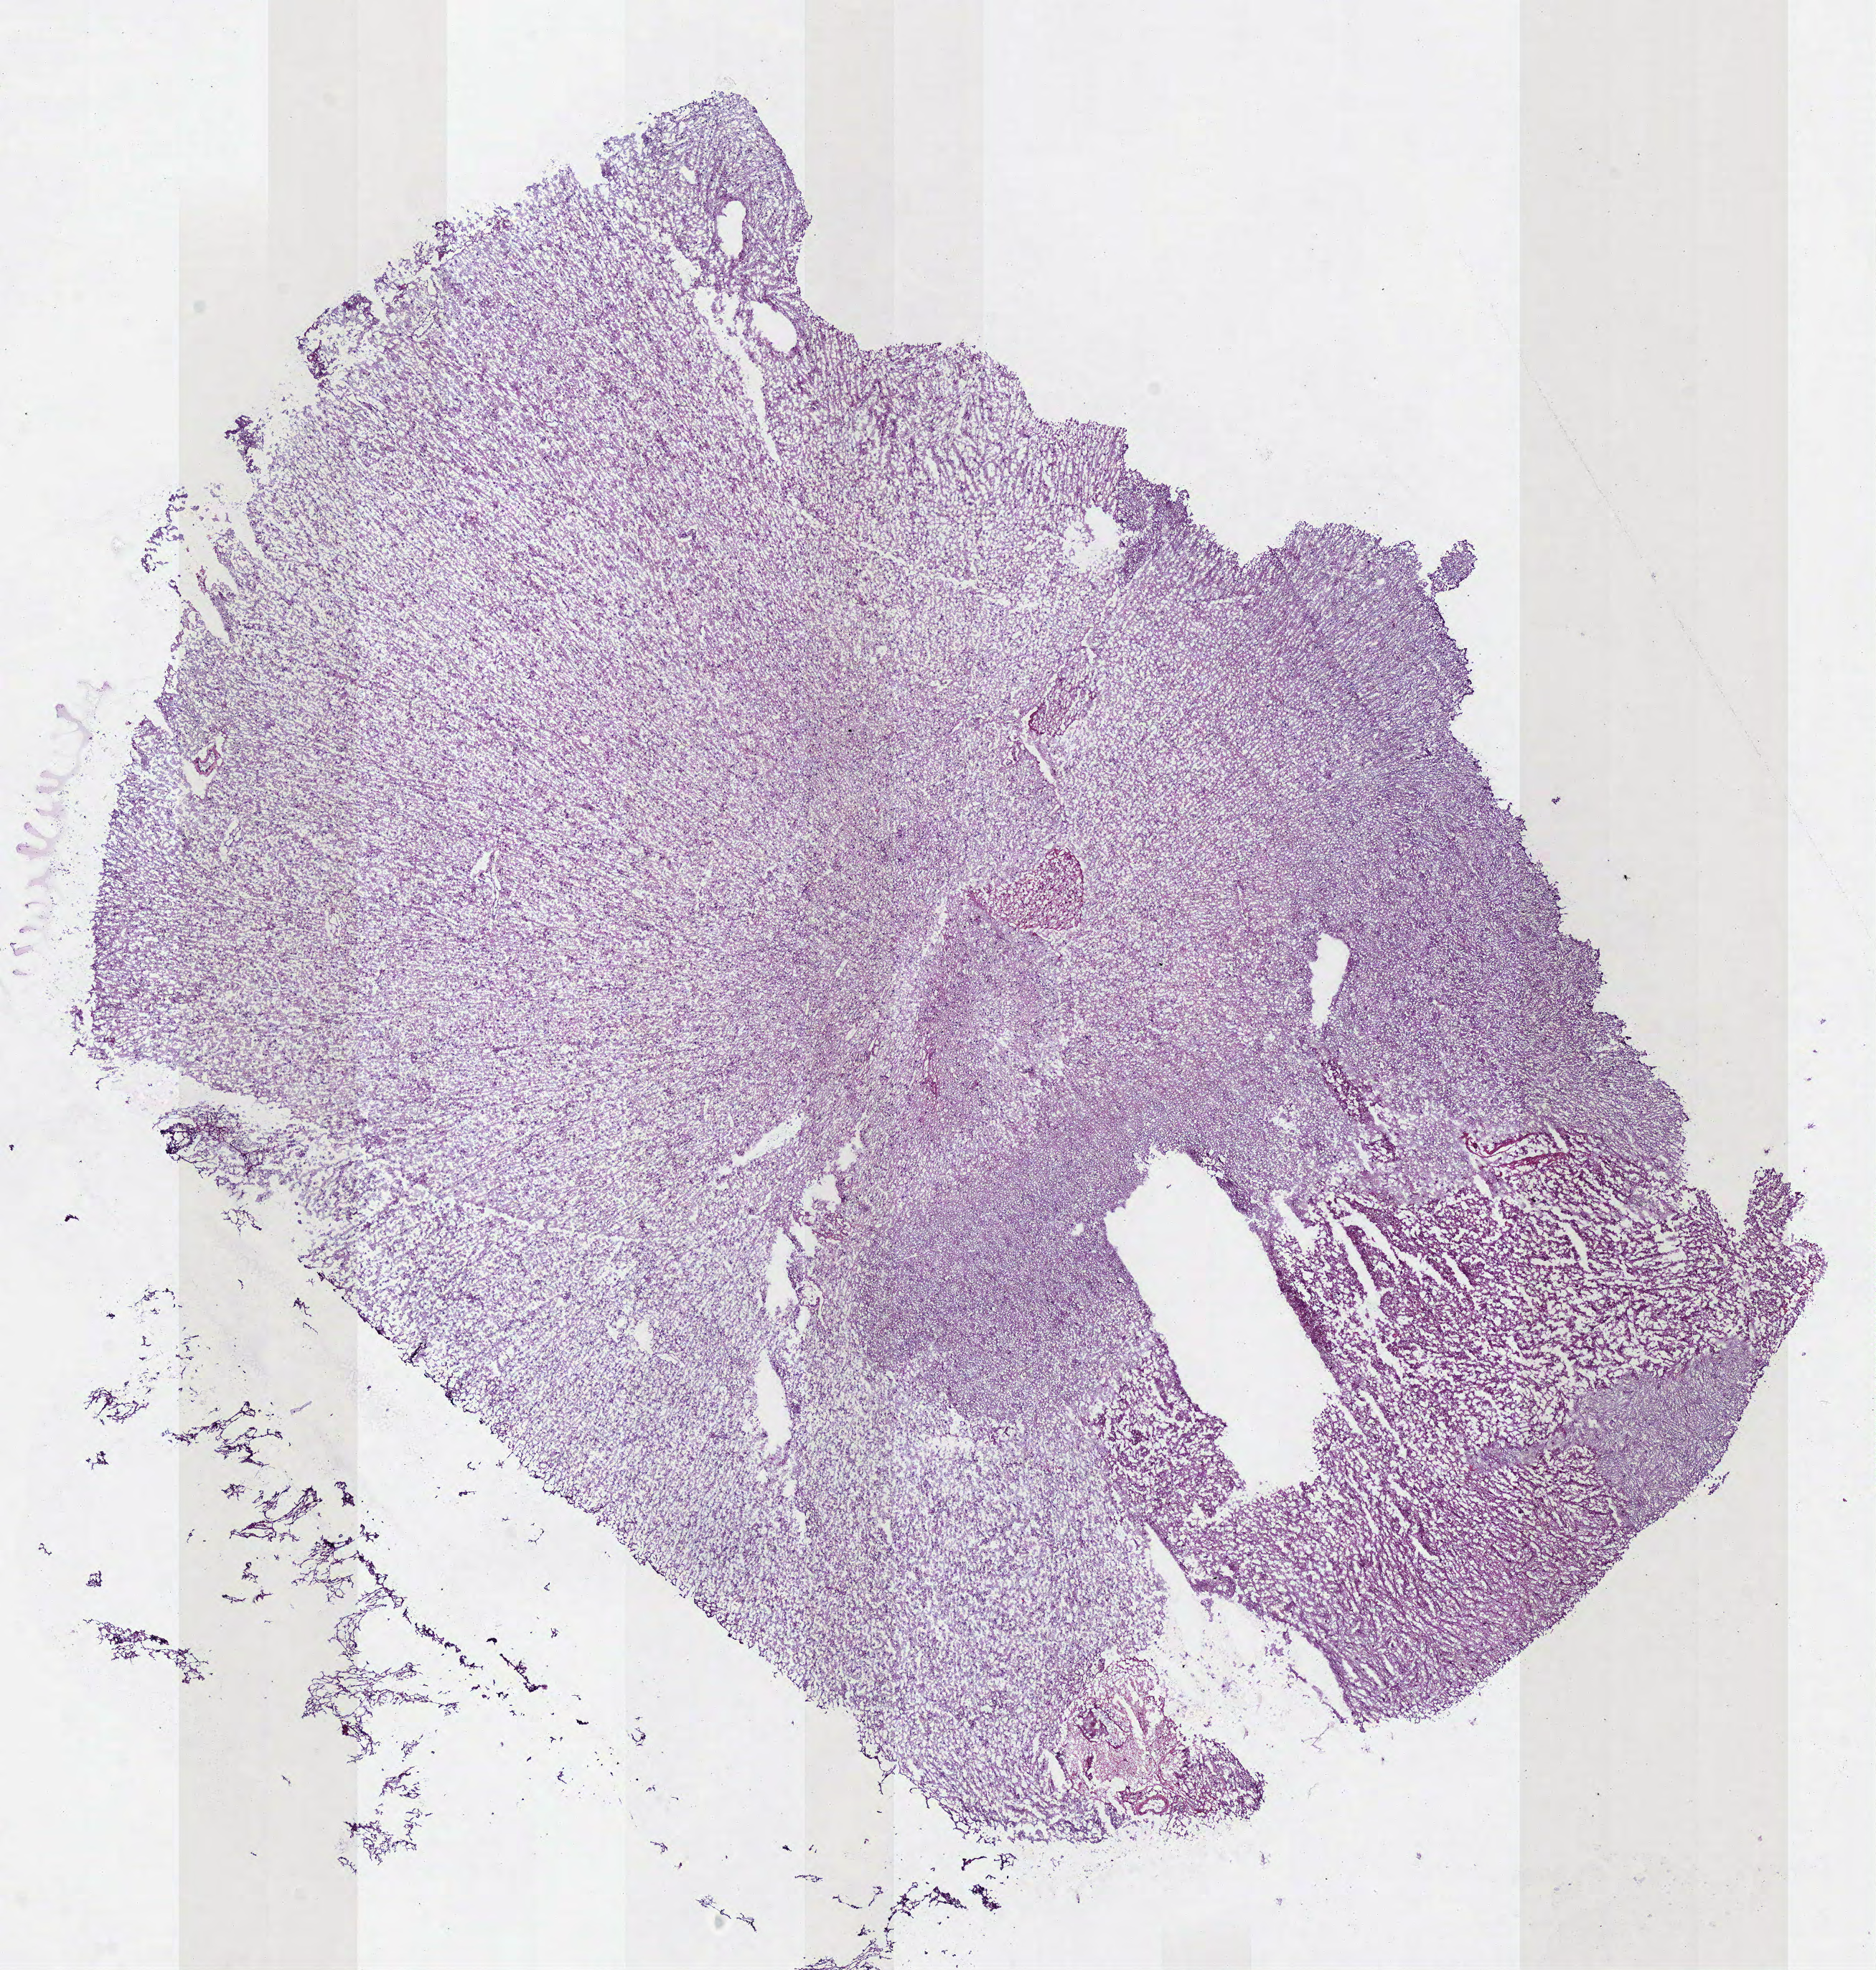
Whole-slide histology image, H&E-stained — low-resolution overview of the scanned area, about 10.3 x 10.8 mm (slide scanned at 40x). Frozen section from the bottom of the tissue portion. Sample: primary tumour, brain. Patient: male, age at initial diagnosis 25 years. Histologic grade: G2 (moderately differentiated). Composition of this section per pathologist review: tumour cells 100%, tumour nuclei 65%, normal cells 0%, stromal cells 0%, necrosis 0%.
* pathologic diagnosis: Mixed glioma (cerebrum)
* laterality: right